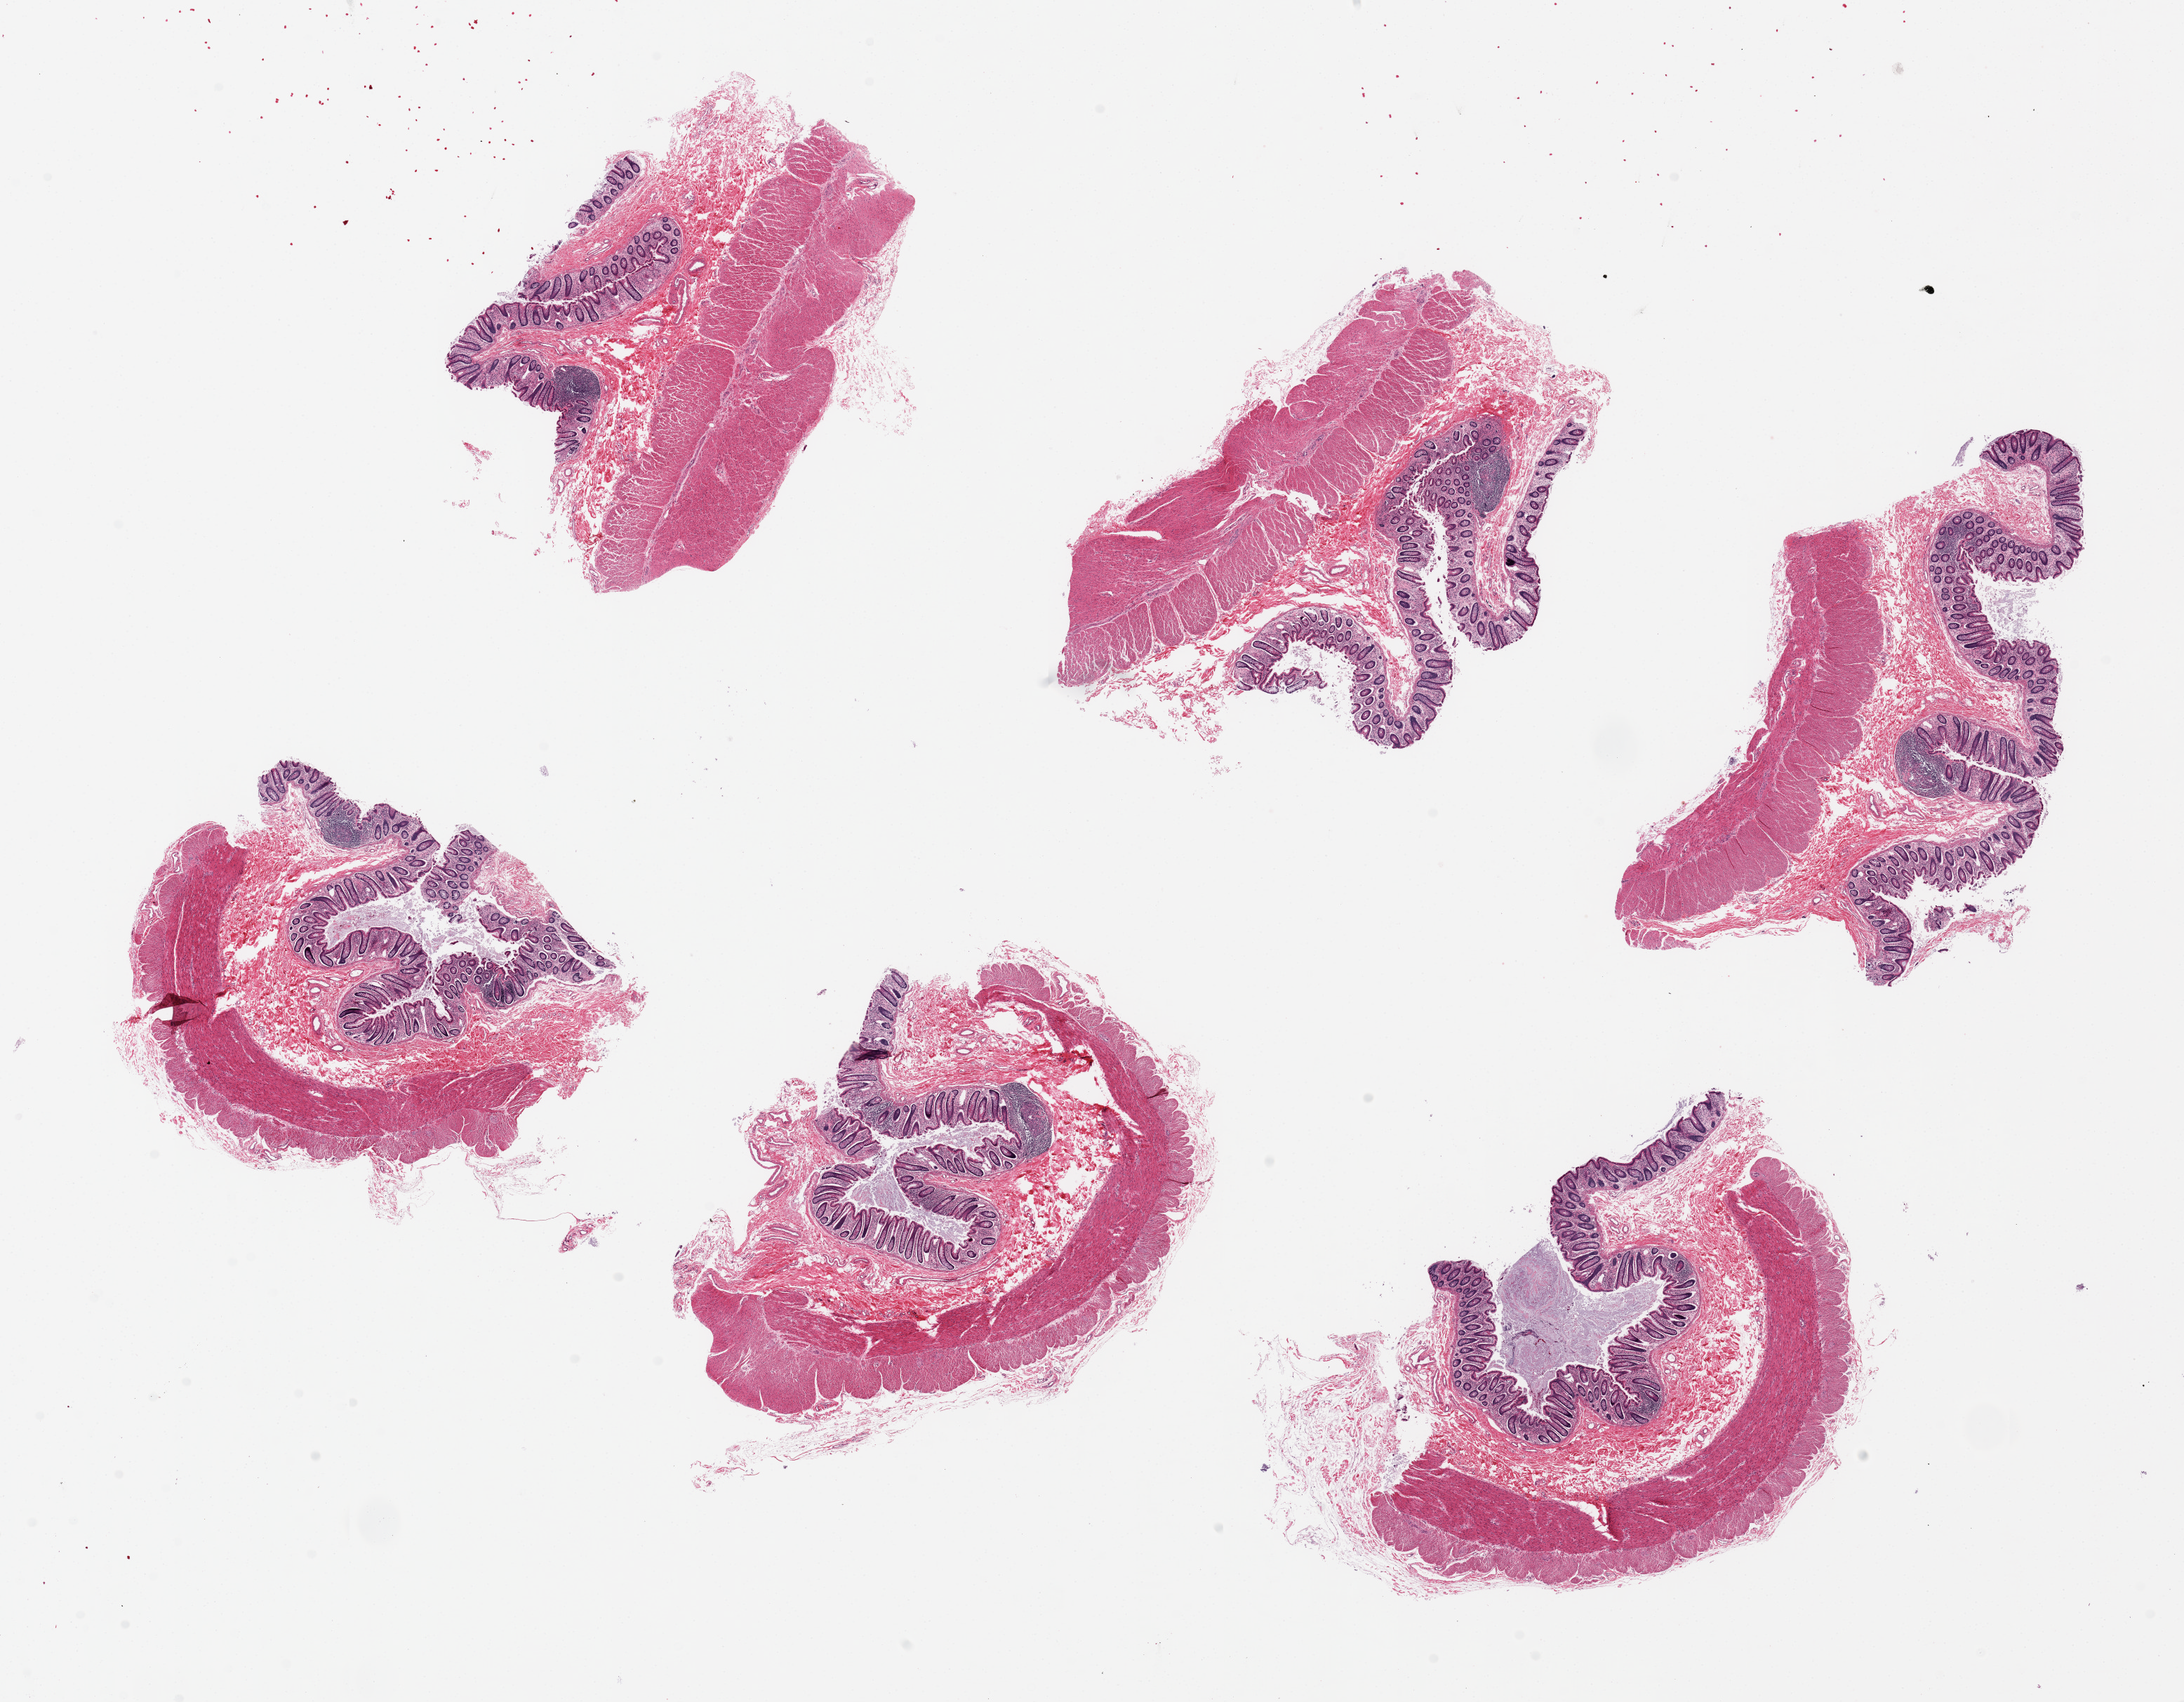
H&E whole-slide image, brightfield — whole scanned area (about 24.6 x 19.2 mm, from a 20x scan) shown as a low-resolution overview. PAXgene-fixed, paraffin-embedded tissue. Sampled site (target tissue): transverse colon. Tissue donor sample. Female donor.
- pathologist's review note for this sample: 6 pieces up to 6x4 mm; good mucosal morphology; full thickness wall